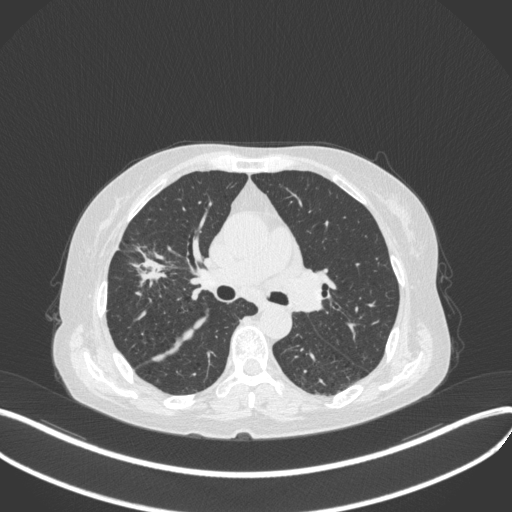
Chest CT, one axial slice; position 242 of 429 along the scan axis; reconstruction kernel B31f; 120 kVp; lung window (W 1500 / L -600 HU); 1 mm slice thickness; 512 × 512 image matrix, field of view 400 × 400 mm. Female patient, age 69 years. Case-level facts recorded for this patient, not image findings: clinical TNM (as recorded): T1b N3 M0.
Structures marked on this image (rectangle marked by the reading radiologist):
- lung tumour (recorded histology: small cell carcinoma): bounding box <123,240,173,293> (left, top, right, bottom; pixels)